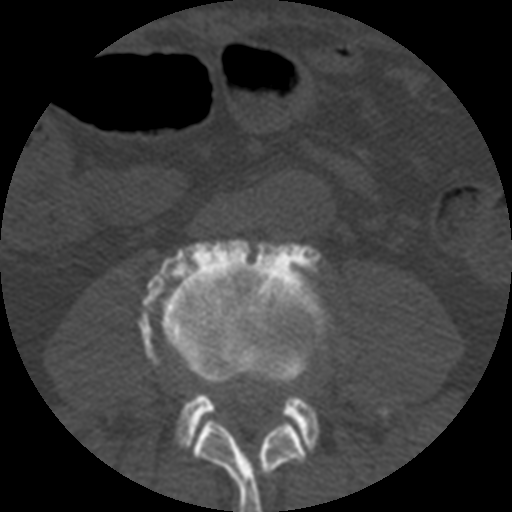
CT including the spine, one axial slice; slice 105 of 508 in the series (ordered by position); reconstruction kernel STANDARD; bone window (W 1800 / L 400 HU); 1.25 mm slice thickness; 512 × 512 image matrix. Patient age 57 years. Case-level facts recorded for this patient, not image findings: primary cancer: prostate.
Structures marked on this image (semi-automatic segmentation, software-assisted and operator-edited):
- L3 vertebra: bounding box [x1, y1, x2, y2] px = [193, 419, 305, 512]
- L4 vertebra: [139, 238, 326, 452]